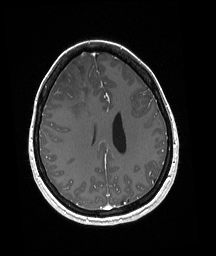
Brain MRI from a brain-tumour surgery series, one axial slice; position 74 of 192 along the scan axis; T1-weighted post-contrast; 1 mm slice thickness; 216 × 256 image matrix. Case-level facts recorded for this patient, not image findings: histopathology: Oligodendroglioma; WHO grade: 3.
Structures marked on this image (expert manual segmentation):
- tumour: bounding box <67,84,86,91> (left, top, right, bottom; pixels)